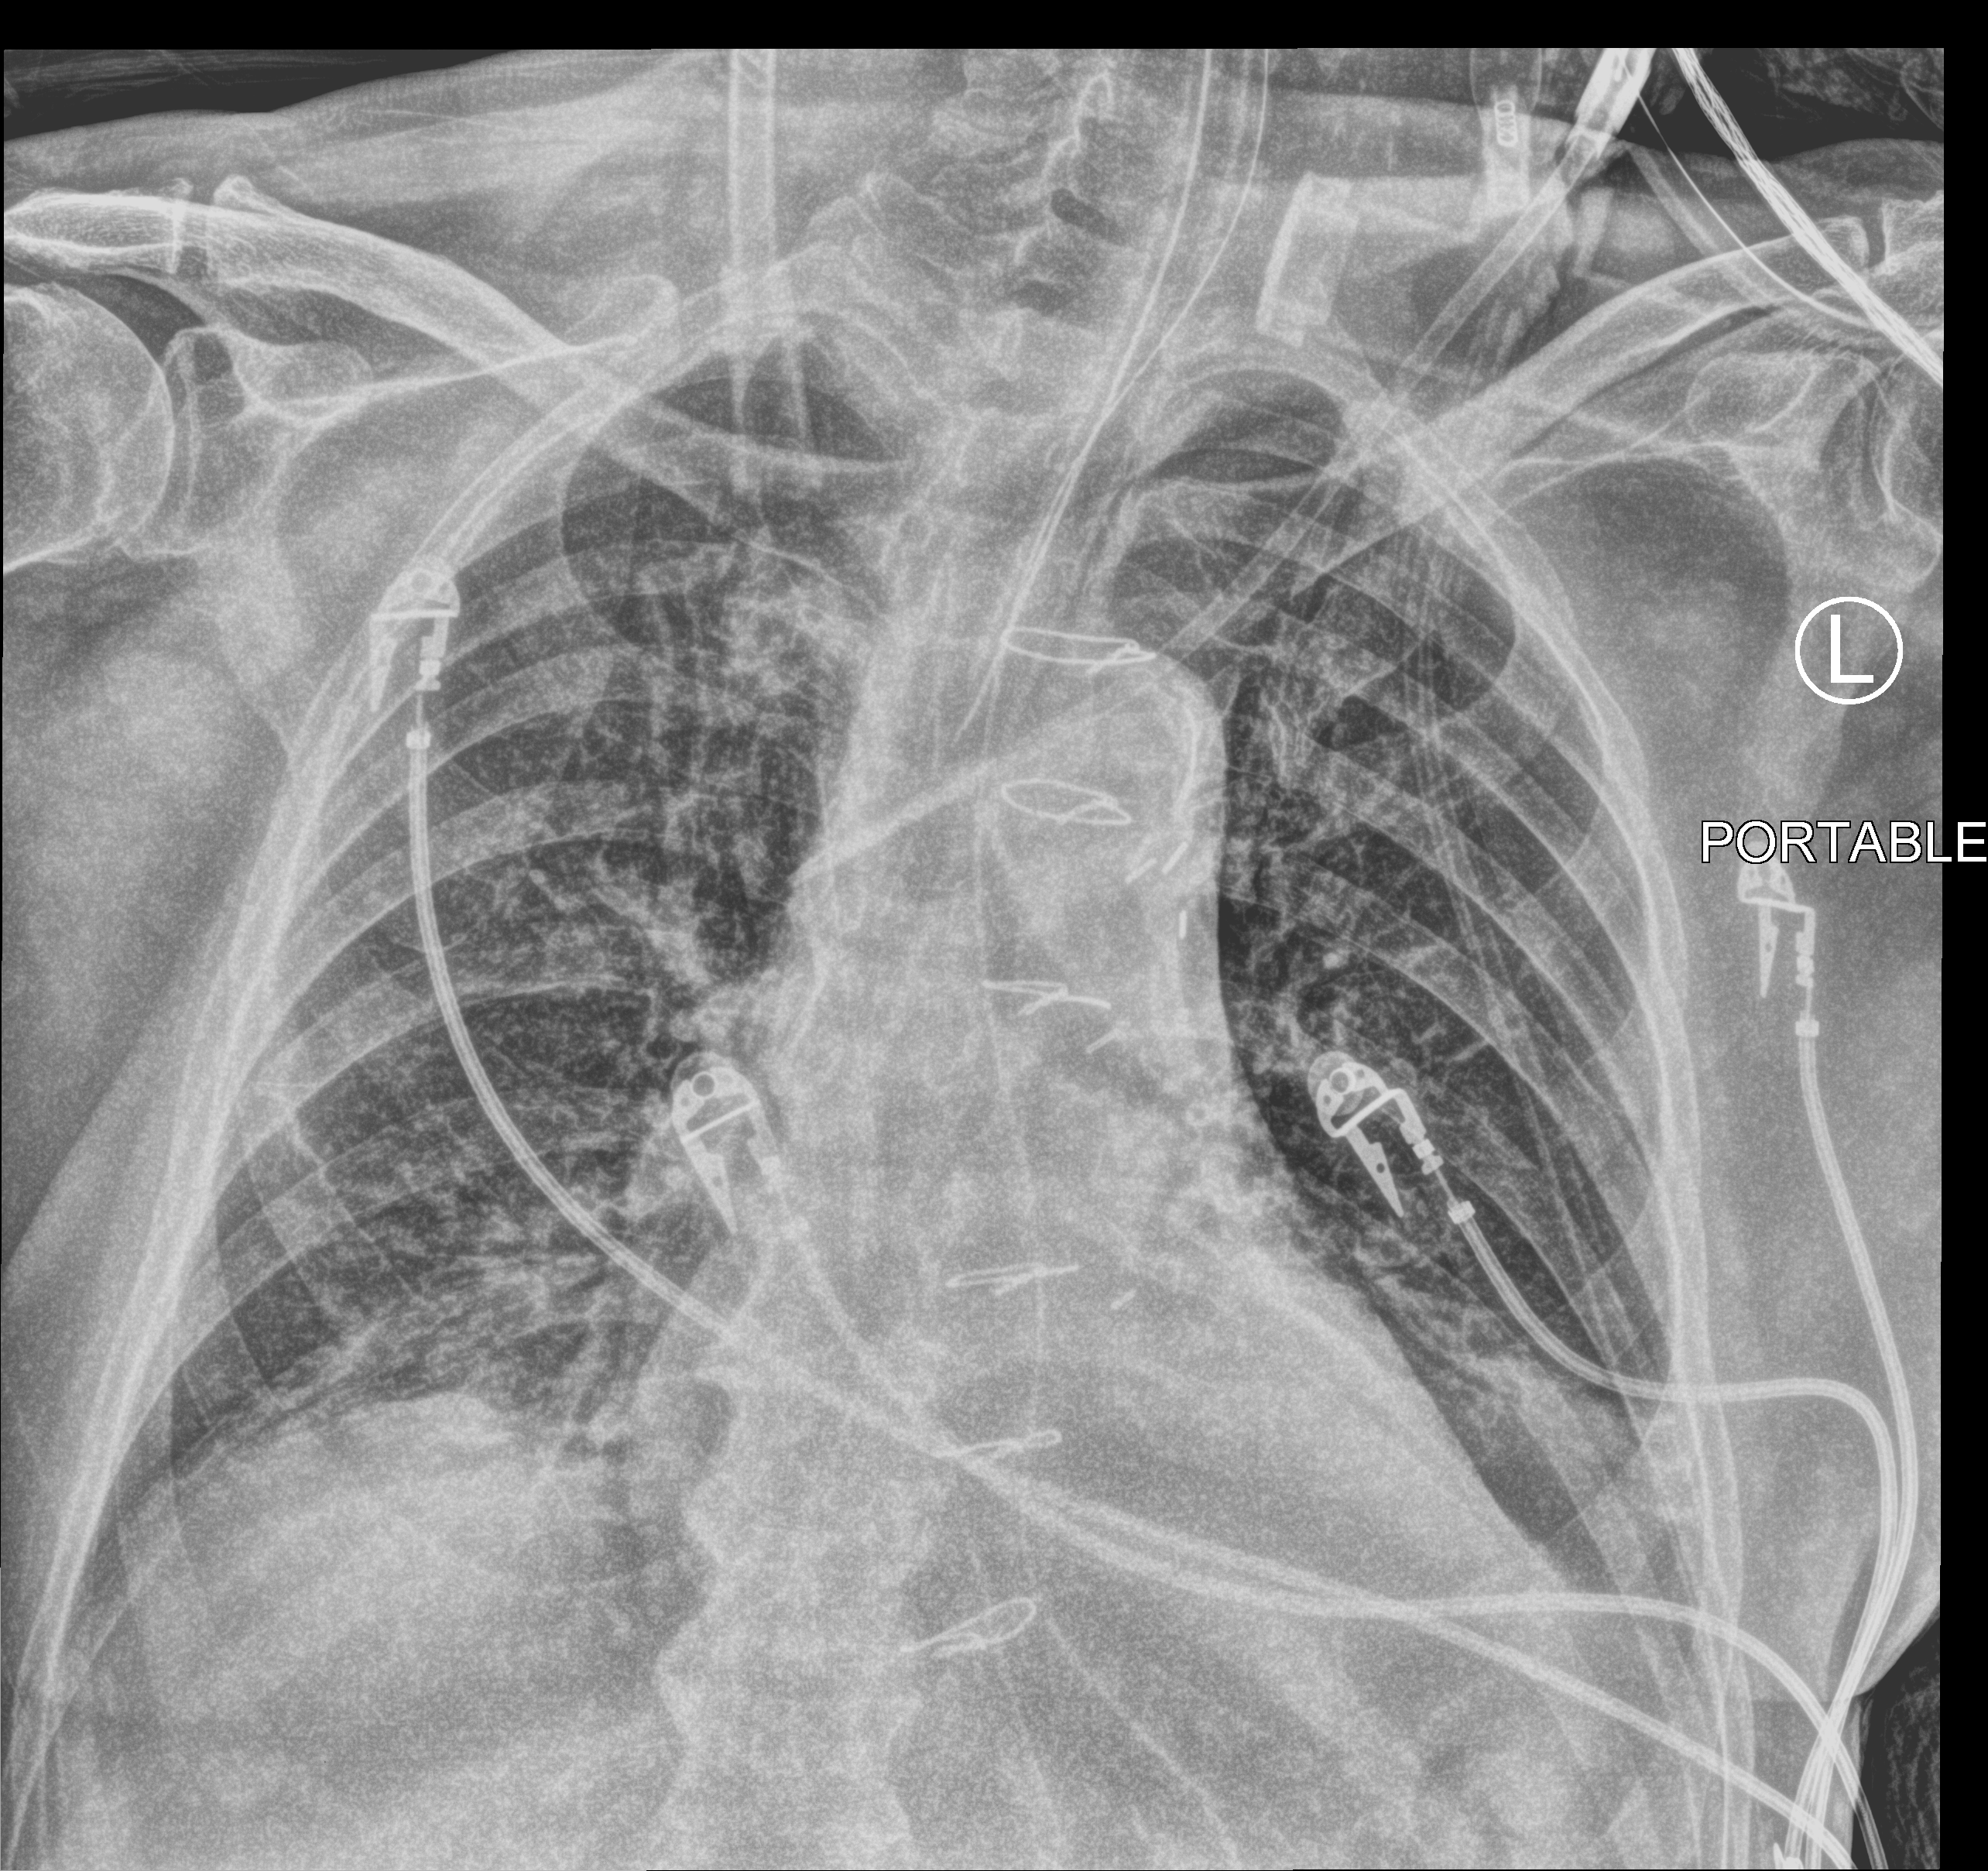
Portable chest radiograph, anteroposterior (AP) projection. Patient hospitalised with COVID-19; male, aged 75–90 years.
From the hospital-stay record, not from the radiograph (when in the stay this image was taken is not recorded):
- admitted to intensive care during this hospital stay: yes